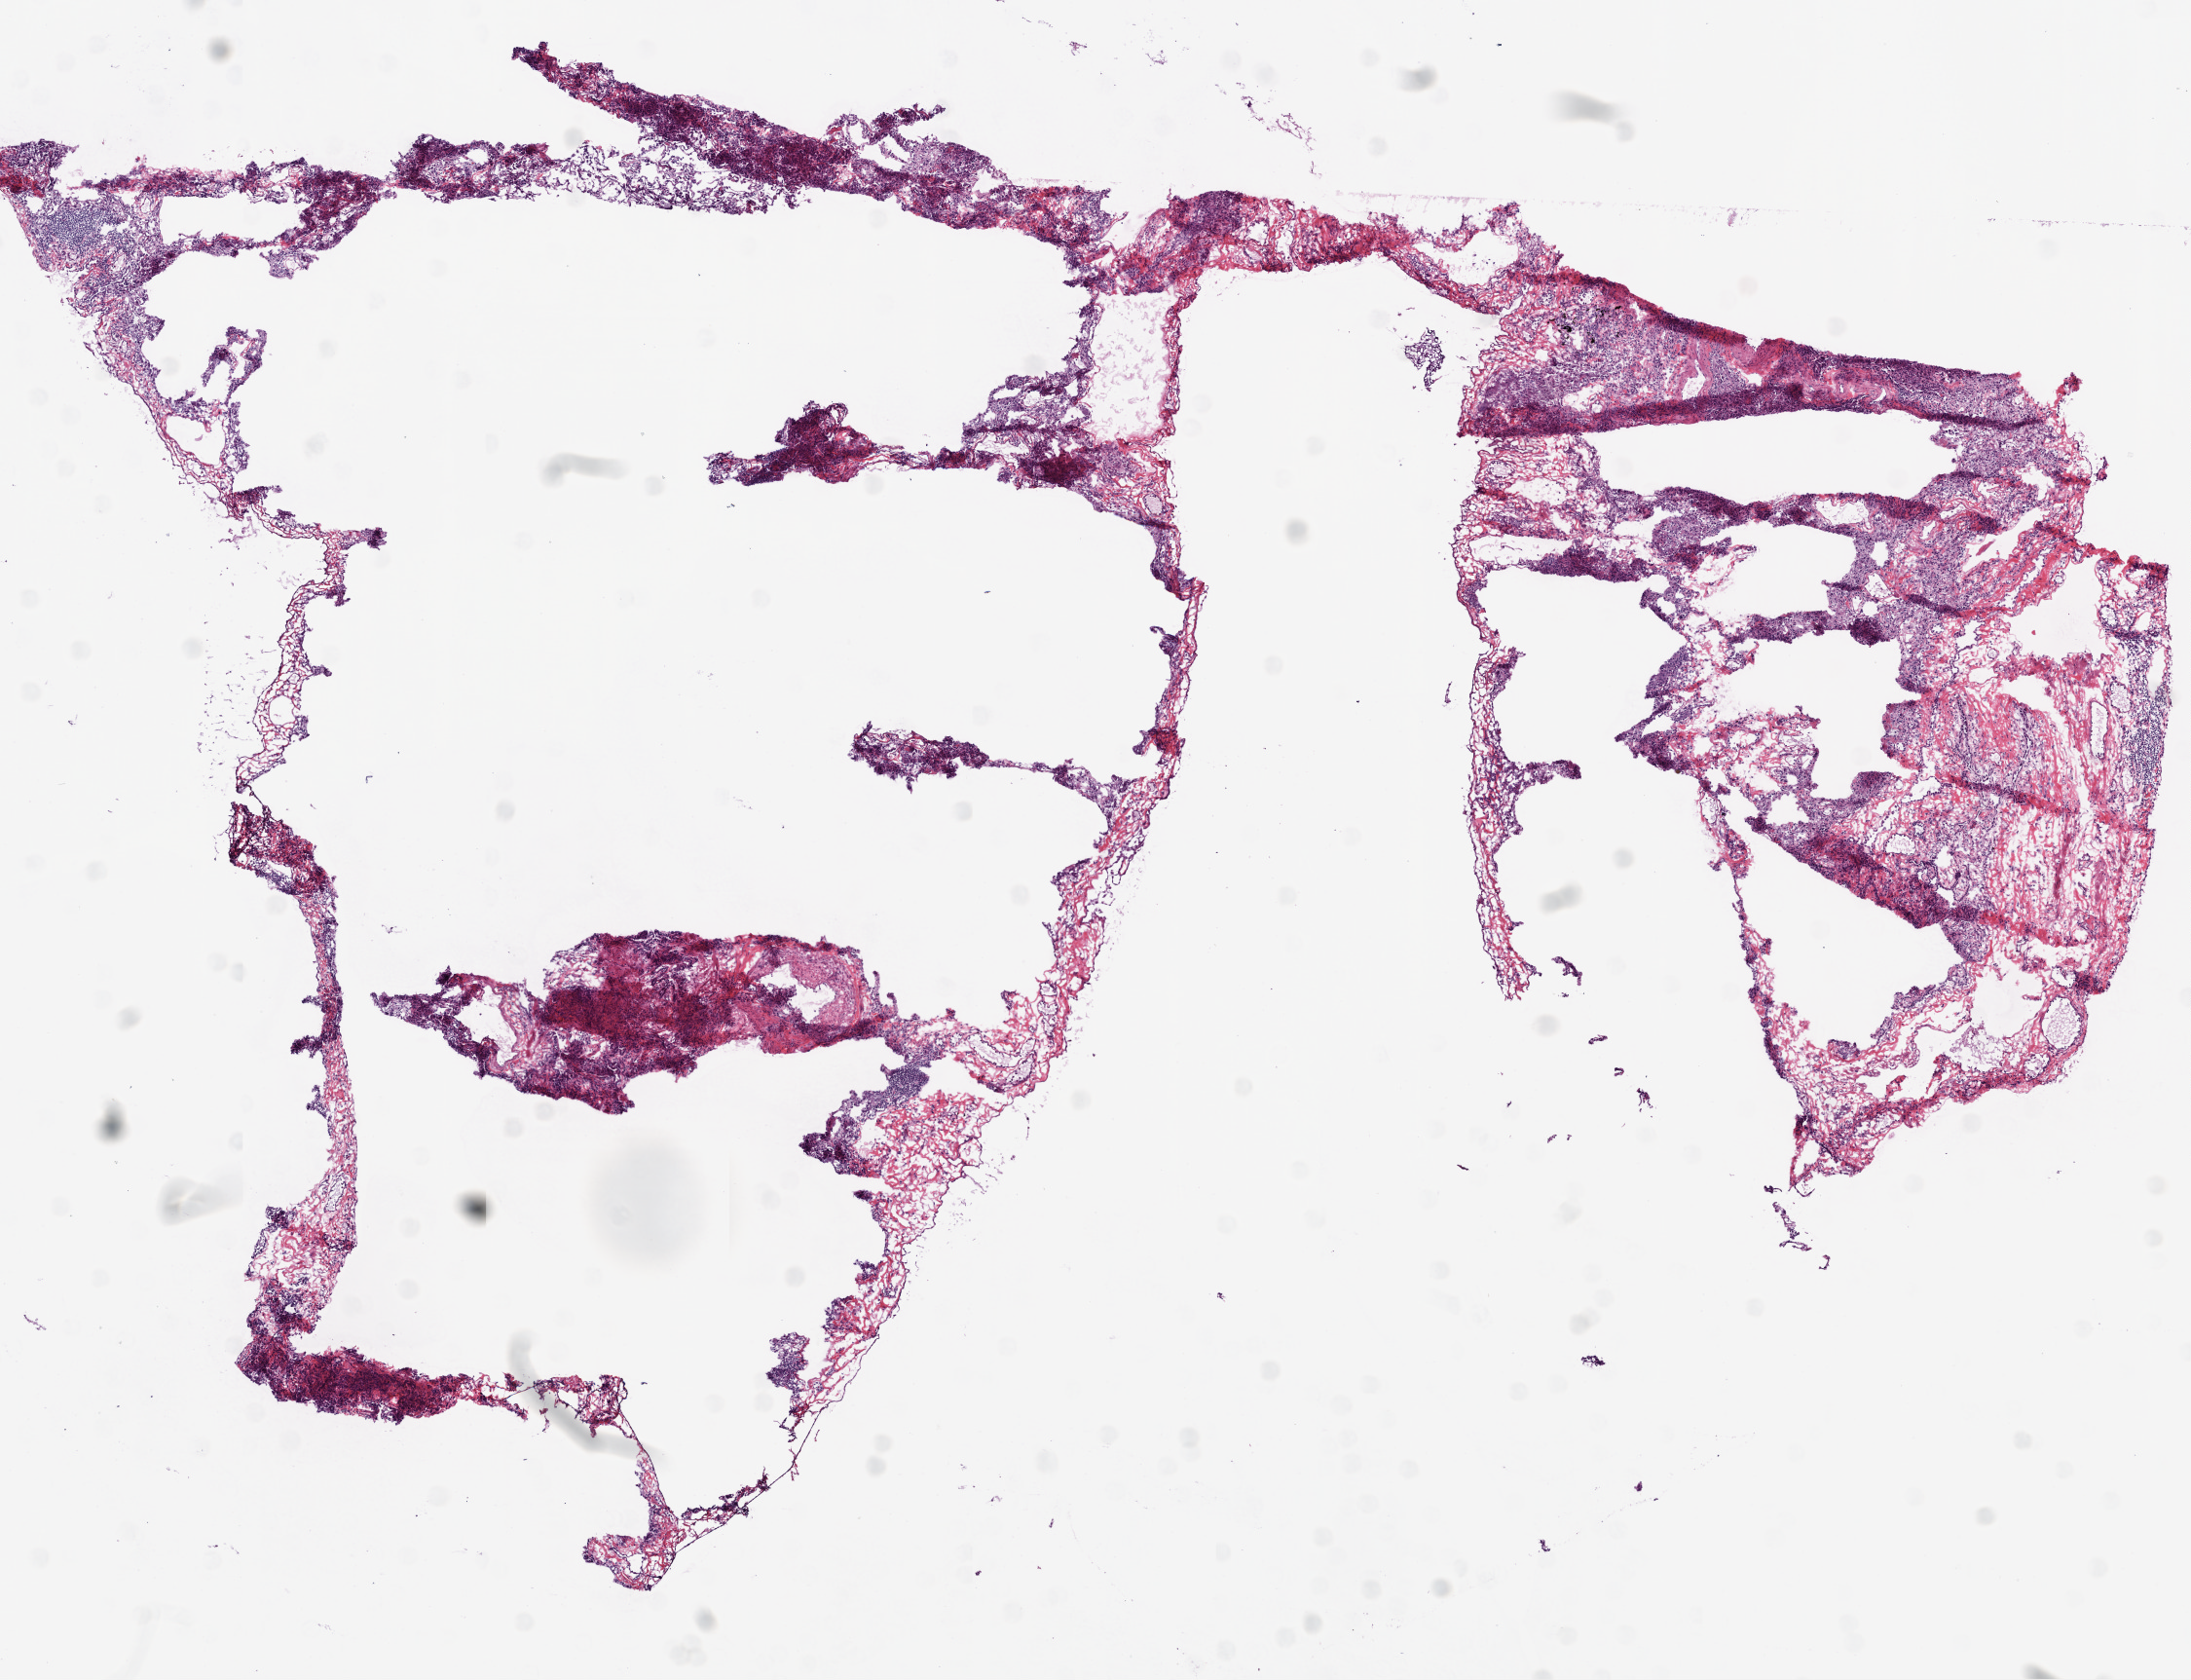
Digitized Hematoxylin and eosin (H&E) stained tissue section (whole slide), a low-resolution overview of the entire scanned area, about 9.0 x 6.9 mm. Frozen section from the bottom of the tissue portion. Sample: solid tissue normal (non-tumour tissue), lung. Male, age 54 years at initial diagnosis.
This section: solid tissue normal (non-tumour) sample from the same patient. Patient diagnosis: Squamous cell carcinoma, NOS.